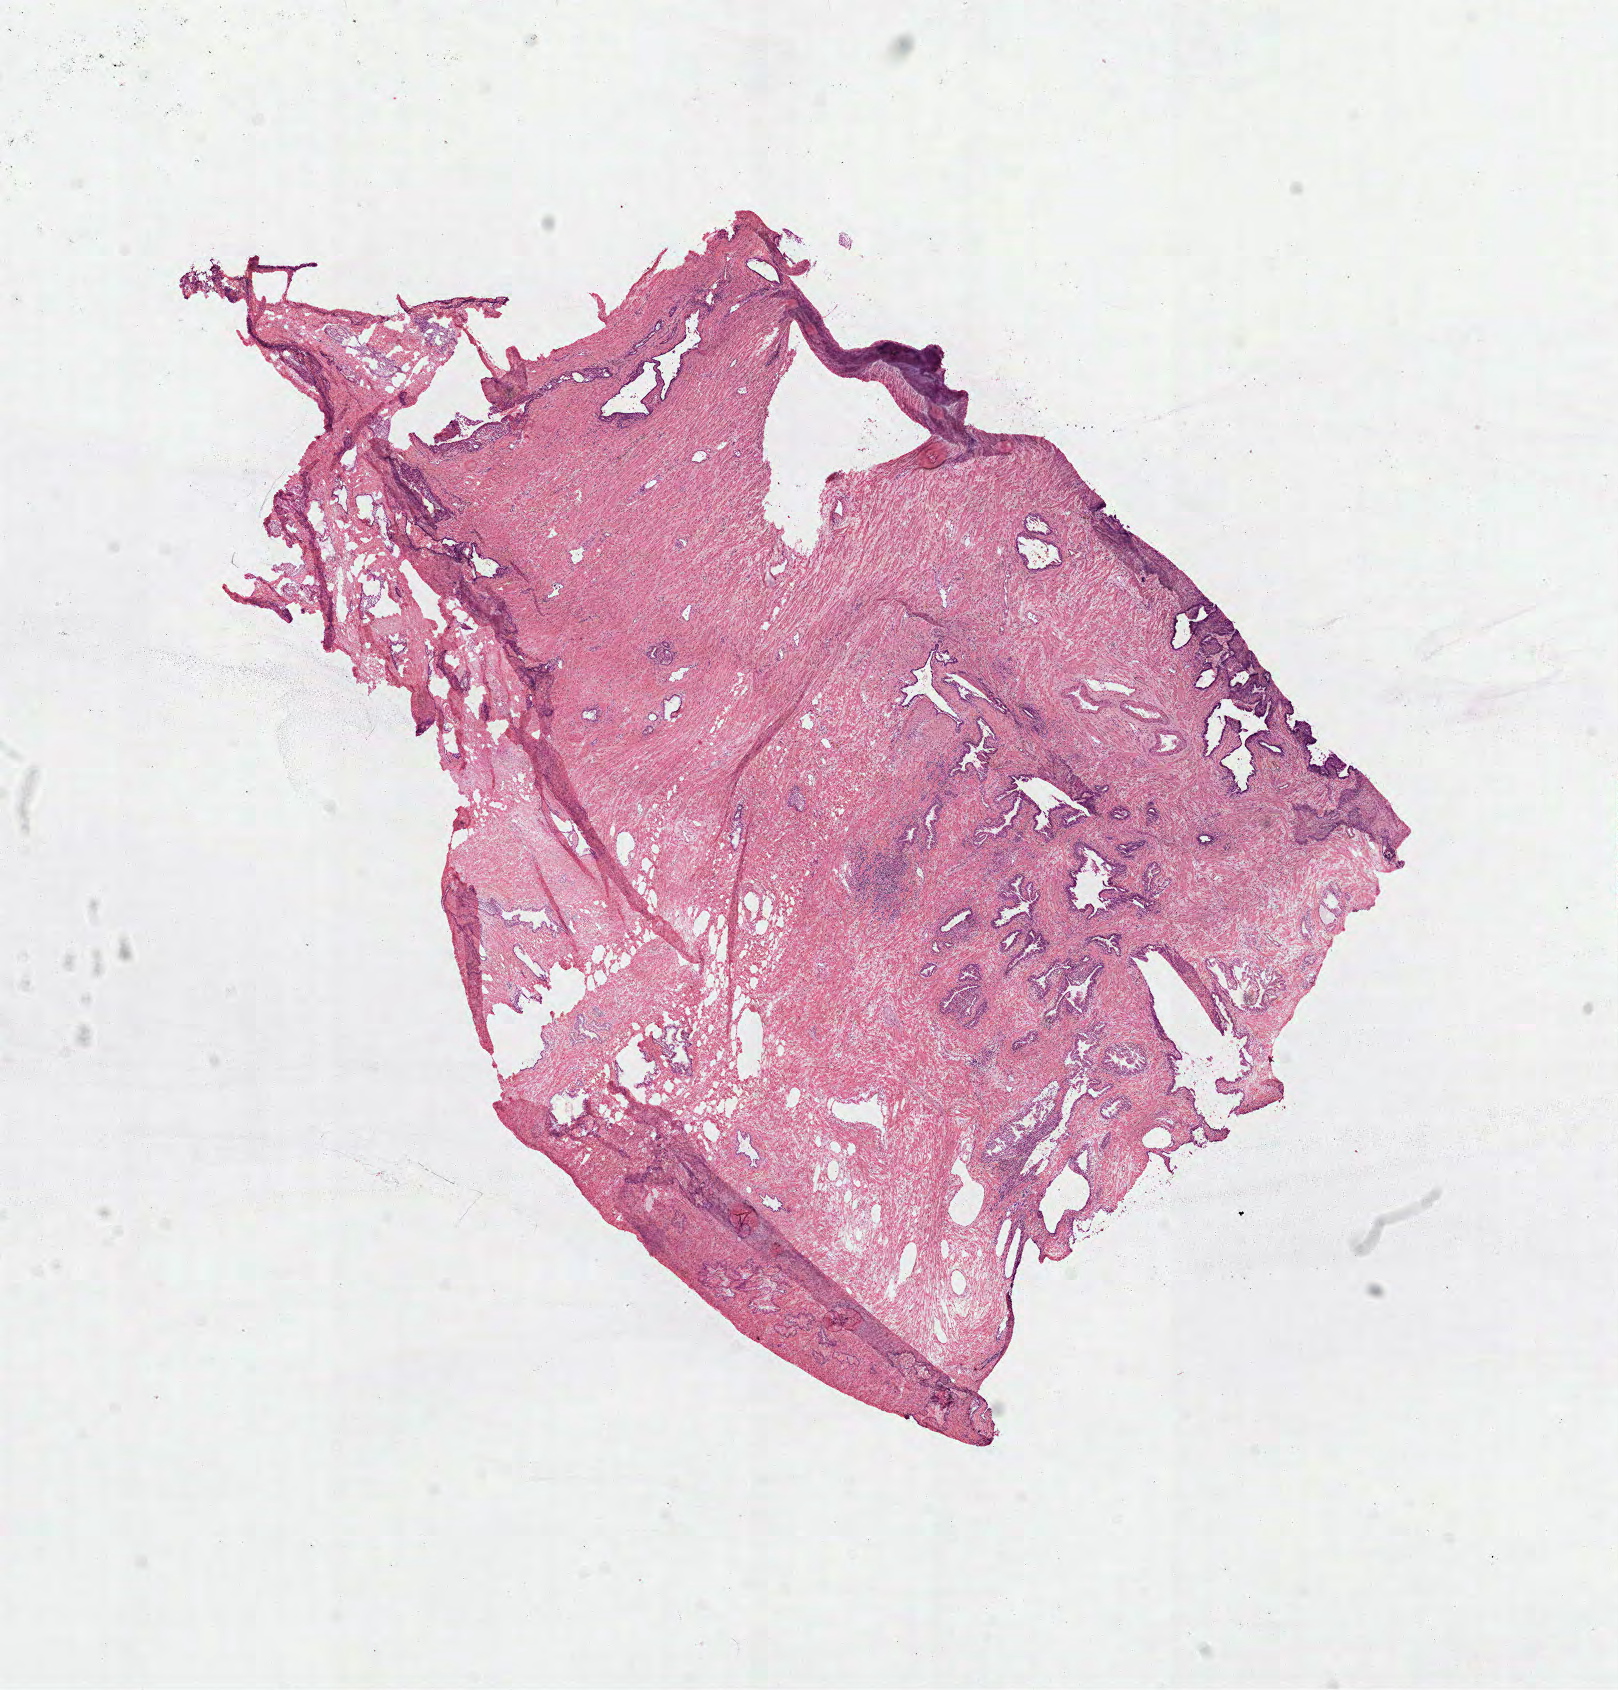
Whole-slide histology image, H&E — a low-resolution overview of the entire scanned area, about 13.1 x 13.6 mm. Frozen section from the top of the tissue portion. Sample: solid tissue normal (non-tumour tissue), prostate. Male patient; age at initial diagnosis 57 years.
This section: solid tissue normal sample (biorepository sample class). Patient diagnosis: Acinar cell carcinoma (prostate gland).